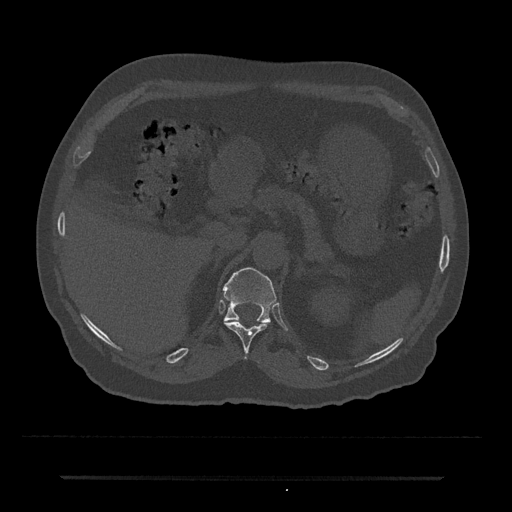
CT including the spine, one axial slice. Position 155 of 797 along the scan axis. Reconstruction kernel Br40s/3. 120 kVp. Bone window (W 1800 / L 400 HU). 0.5 mm slice thickness. 512 × 512 image matrix. Male patient, age 69 years. Case-level facts recorded for this patient, not image findings: primary cancer: prostate.
Annotated regions visible in this slice (semi-automatically segmented with operator editing):
- T11 vertebra: bounding box (x1, y1, x2, y2) in pixels: (224, 321, 267, 353)
- T12 vertebra: (222, 267, 276, 323)